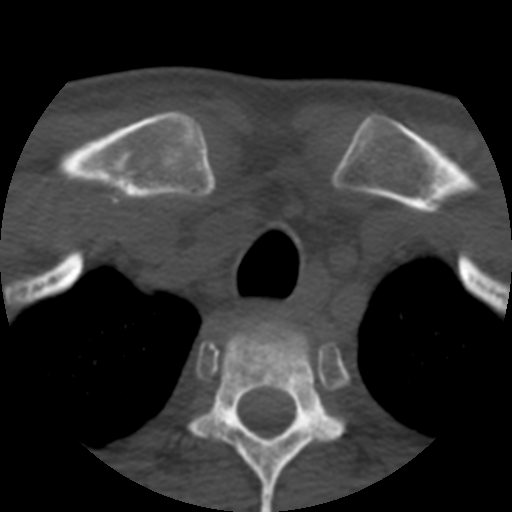
CT including the spine, one axial slice; slice 432 of 508 in the series (ordered by position); bone window (W 1800 / L 400 HU); 512 × 512 image matrix, field of view 160 × 160 mm. Patient age 57 years. From the clinical record (not read from this slice): primary cancer: prostate.
Outlined on this slice (semi-automatically segmented with operator editing):
- T1 vertebra: box from (x=305, y=335) to (x=309, y=345) px
- T2 vertebra: (x=191, y=319)–(x=344, y=512)